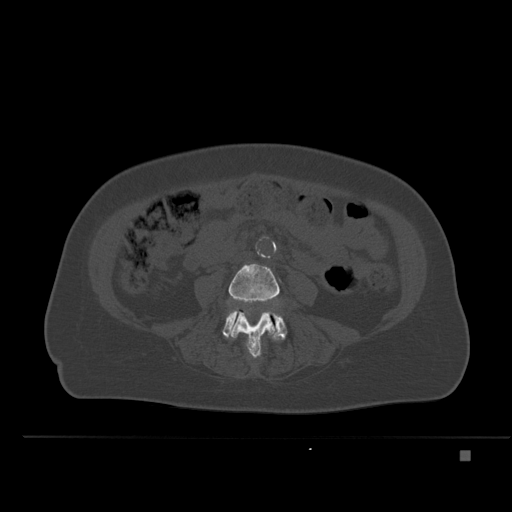
CT including the spine, one axial slice. Position 174 of 477 along the scan axis. Bone window (W 1800 / L 400 HU). 512 × 512 image matrix, field of view 422 × 422 mm. Patient: female, 74 years. From the clinical record (not read from this slice): primary cancer: colon.
Outlined on this slice (semi-automatic segmentation, software-assisted and operator-edited):
- L4 vertebra: bounding box (x1, y1, x2, y2) in pixels: (229, 263, 280, 358)
- L5 vertebra: (222, 307, 287, 341)